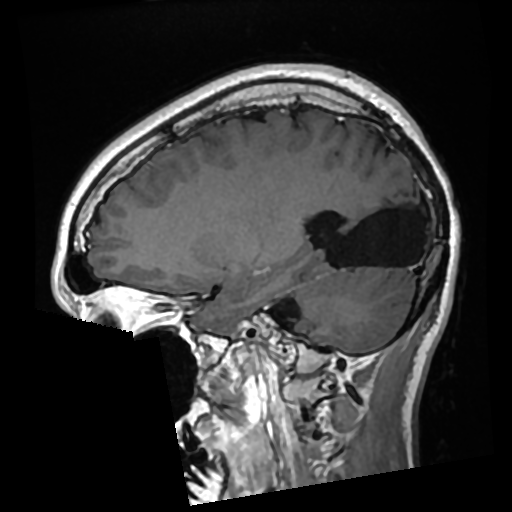
Brain MRI from a brain-tumour surgery series, one sagittal slice; slice 105 of 276 in the series (ordered by position); T1-weighted post-contrast; 0.7 mm slice thickness; 512 × 512 image matrix, field of view 250 × 250 mm. Case-level facts recorded for this patient, not image findings: histopathology: Glioma with ependymal features; WHO grade: 2; tumour location: Left Parietal.
Outlined on this slice (outlined manually by an expert reader):
- previous resection cavity: box from (x=327, y=184) to (x=424, y=266) px